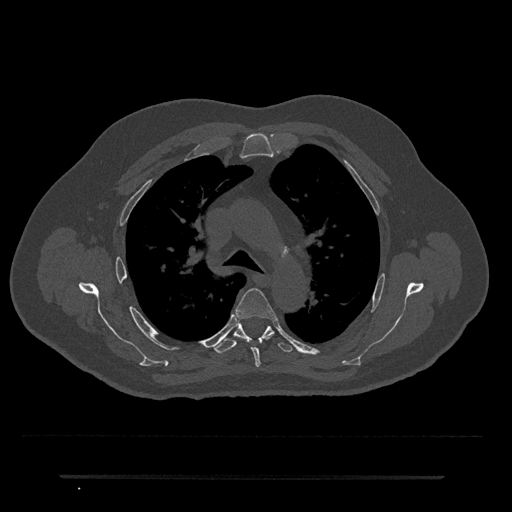
CT including the spine, one axial slice; slice 507 of 797 in the series (ordered by position); reconstruction kernel Br40s/3; 120 kVp; bone window (W 1800 / L 400 HU); 0.5 mm slice thickness; 512 × 512 image matrix, field of view 437 × 437 mm. Patient: male, 69 years. From the clinical record (not read from this slice): primary cancer: prostate.
Structures marked on this image (semi-automatic segmentation, software-assisted and operator-edited):
- T4 vertebra: bounding box (x1, y1, x2, y2) in pixels: (236, 288, 276, 367)
- T5 vertebra: (212, 321, 293, 354)